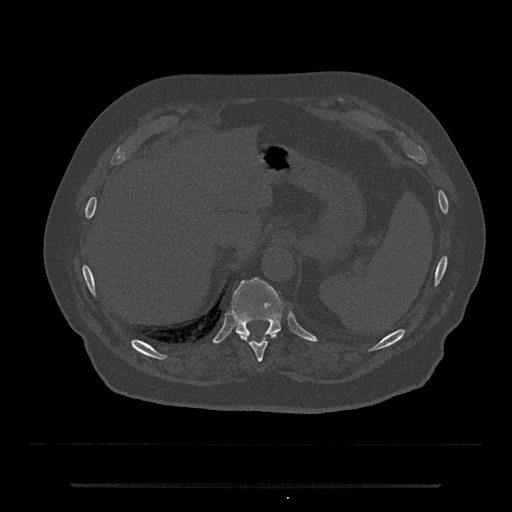
CT including the spine, one axial slice. Slice 677 of 797 in the series (ordered by position). 120 kVp. Bone window (W 1800 / L 400 HU). 0.5 mm slice thickness. 512 × 512 image matrix, field of view 434 × 434 mm. Patient: male, 80 years. From the clinical record (not read from this slice): primary cancer: prostate; vertebrae with lytic lesions (as recorded): L1, T11.
Outlined on this slice (semi-automatically segmented with operator editing):
- T10 vertebra: bounding box <240,333,277,362> (left, top, right, bottom; pixels)
- T11 vertebra: <231,277,284,337>